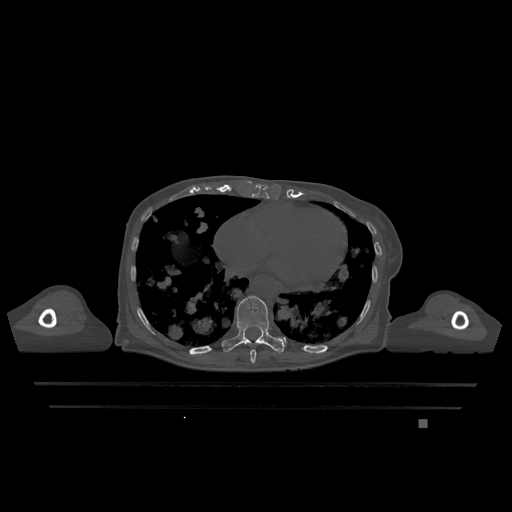
CT including the spine, one axial slice; slice 654 of 1317 in the series (ordered by position); bone window (W 1800 / L 400 HU); 0.5 mm slice thickness; 512 × 512 image matrix, field of view 500 × 500 mm. Patient: female, 74 years. From the clinical record (not read from this slice): primary cancer: lung; vertebrae with lytic lesions (as recorded): T1, T4, T5, T6, L4, L5.
Outlined on this slice (semi-automatic segmentation, software-assisted and operator-edited):
- T10 vertebra: bounding box <222,296,286,353> (left, top, right, bottom; pixels)
- T9 vertebra: <250,349,257,363>